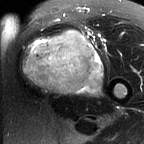
MRI of an extremity soft-tissue mass, one axial slice. T2-weighted fat-saturated. MR volume resampled by the dataset authors to the PET/CT grid (not the native acquisition matrix). 3.27 mm slice thickness. 144 × 144 image matrix, field of view 141 × 141 mm. Female patient. Case-level facts recorded for this patient, not image findings: histological type: pleiomorphic leiomyosarcoma; grade: intermediate; site of the primary tumour: left thigh.
Outlined on this slice (expert contour drawn on MRI and transferred to this co-registered scan by the dataset authors):
- gross tumour volume including surrounding oedema: bounding box [x1, y1, x2, y2] px = [22, 28, 103, 96]
- gross tumour volume (mass): [22, 28, 103, 96]